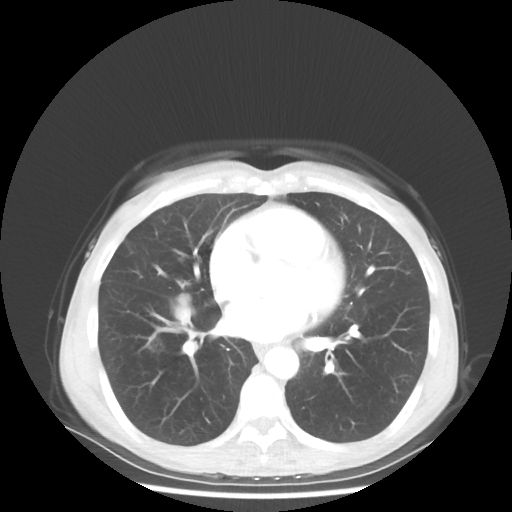
Chest CT, one axial slice; slice 25 of 56 in the series (ordered by position); lung window (W 1500 / L -600 HU); 512 × 512 image matrix. Patient: female, 57 years. Case-level facts recorded for this patient, not image findings: clinical TNM (as recorded): T1c N3 M1a; histopathological grade: G3.
Structures marked on this image (bounding box drawn by a radiologist):
- lung tumour (recorded histology: adenocarcinoma): box from (x=174, y=298) to (x=191, y=328) px